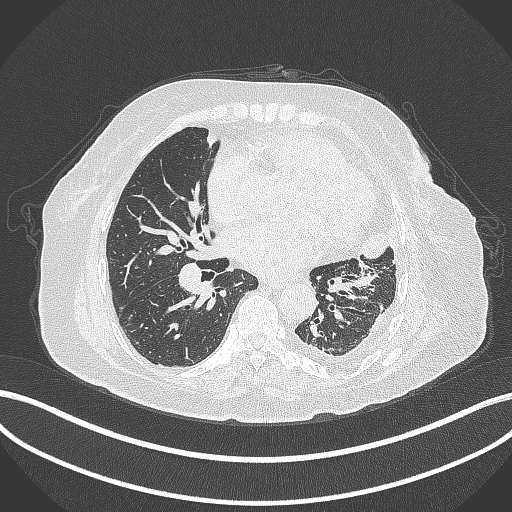
Chest CT, one axial slice; position 166 of 399 along the scan axis; 120 kVp; lung window (W 1500 / L -600 HU); 512 × 512 image matrix, field of view 400 × 400 mm. Female patient, age 75 years. From the clinical record (not read from this slice): clinical TNM (as recorded): T3 N3 M1.
Structures marked on this image (rectangle marked by the reading radiologist):
- lung tumour (recorded histology: adenocarcinoma): bounding box [x1, y1, x2, y2] px = [355, 222, 398, 266]